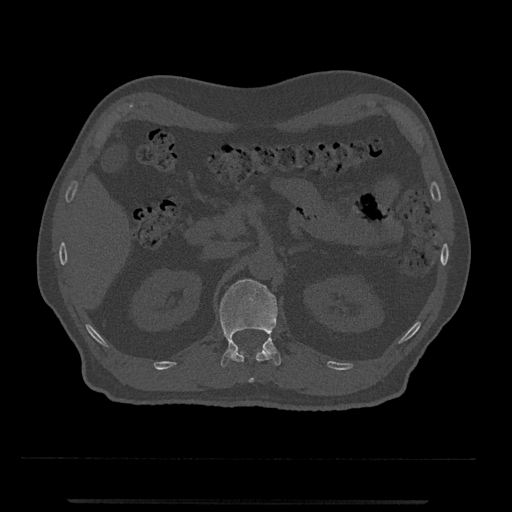
CT including the spine, one axial slice; slice 362 of 797 in the series (ordered by position); reconstruction kernel Br40s/3; bone window (W 1800 / L 400 HU); 0.5 mm slice thickness; 512 × 512 image matrix, field of view 419 × 419 mm. Patient: male, 63 years. From the clinical record (not read from this slice): primary cancer: prostate.
Structures marked on this image (semi-automatic segmentation, software-assisted and operator-edited):
- L1 vertebra: bounding box [x1, y1, x2, y2] px = [219, 279, 281, 368]
- T12 vertebra: [231, 348, 271, 383]